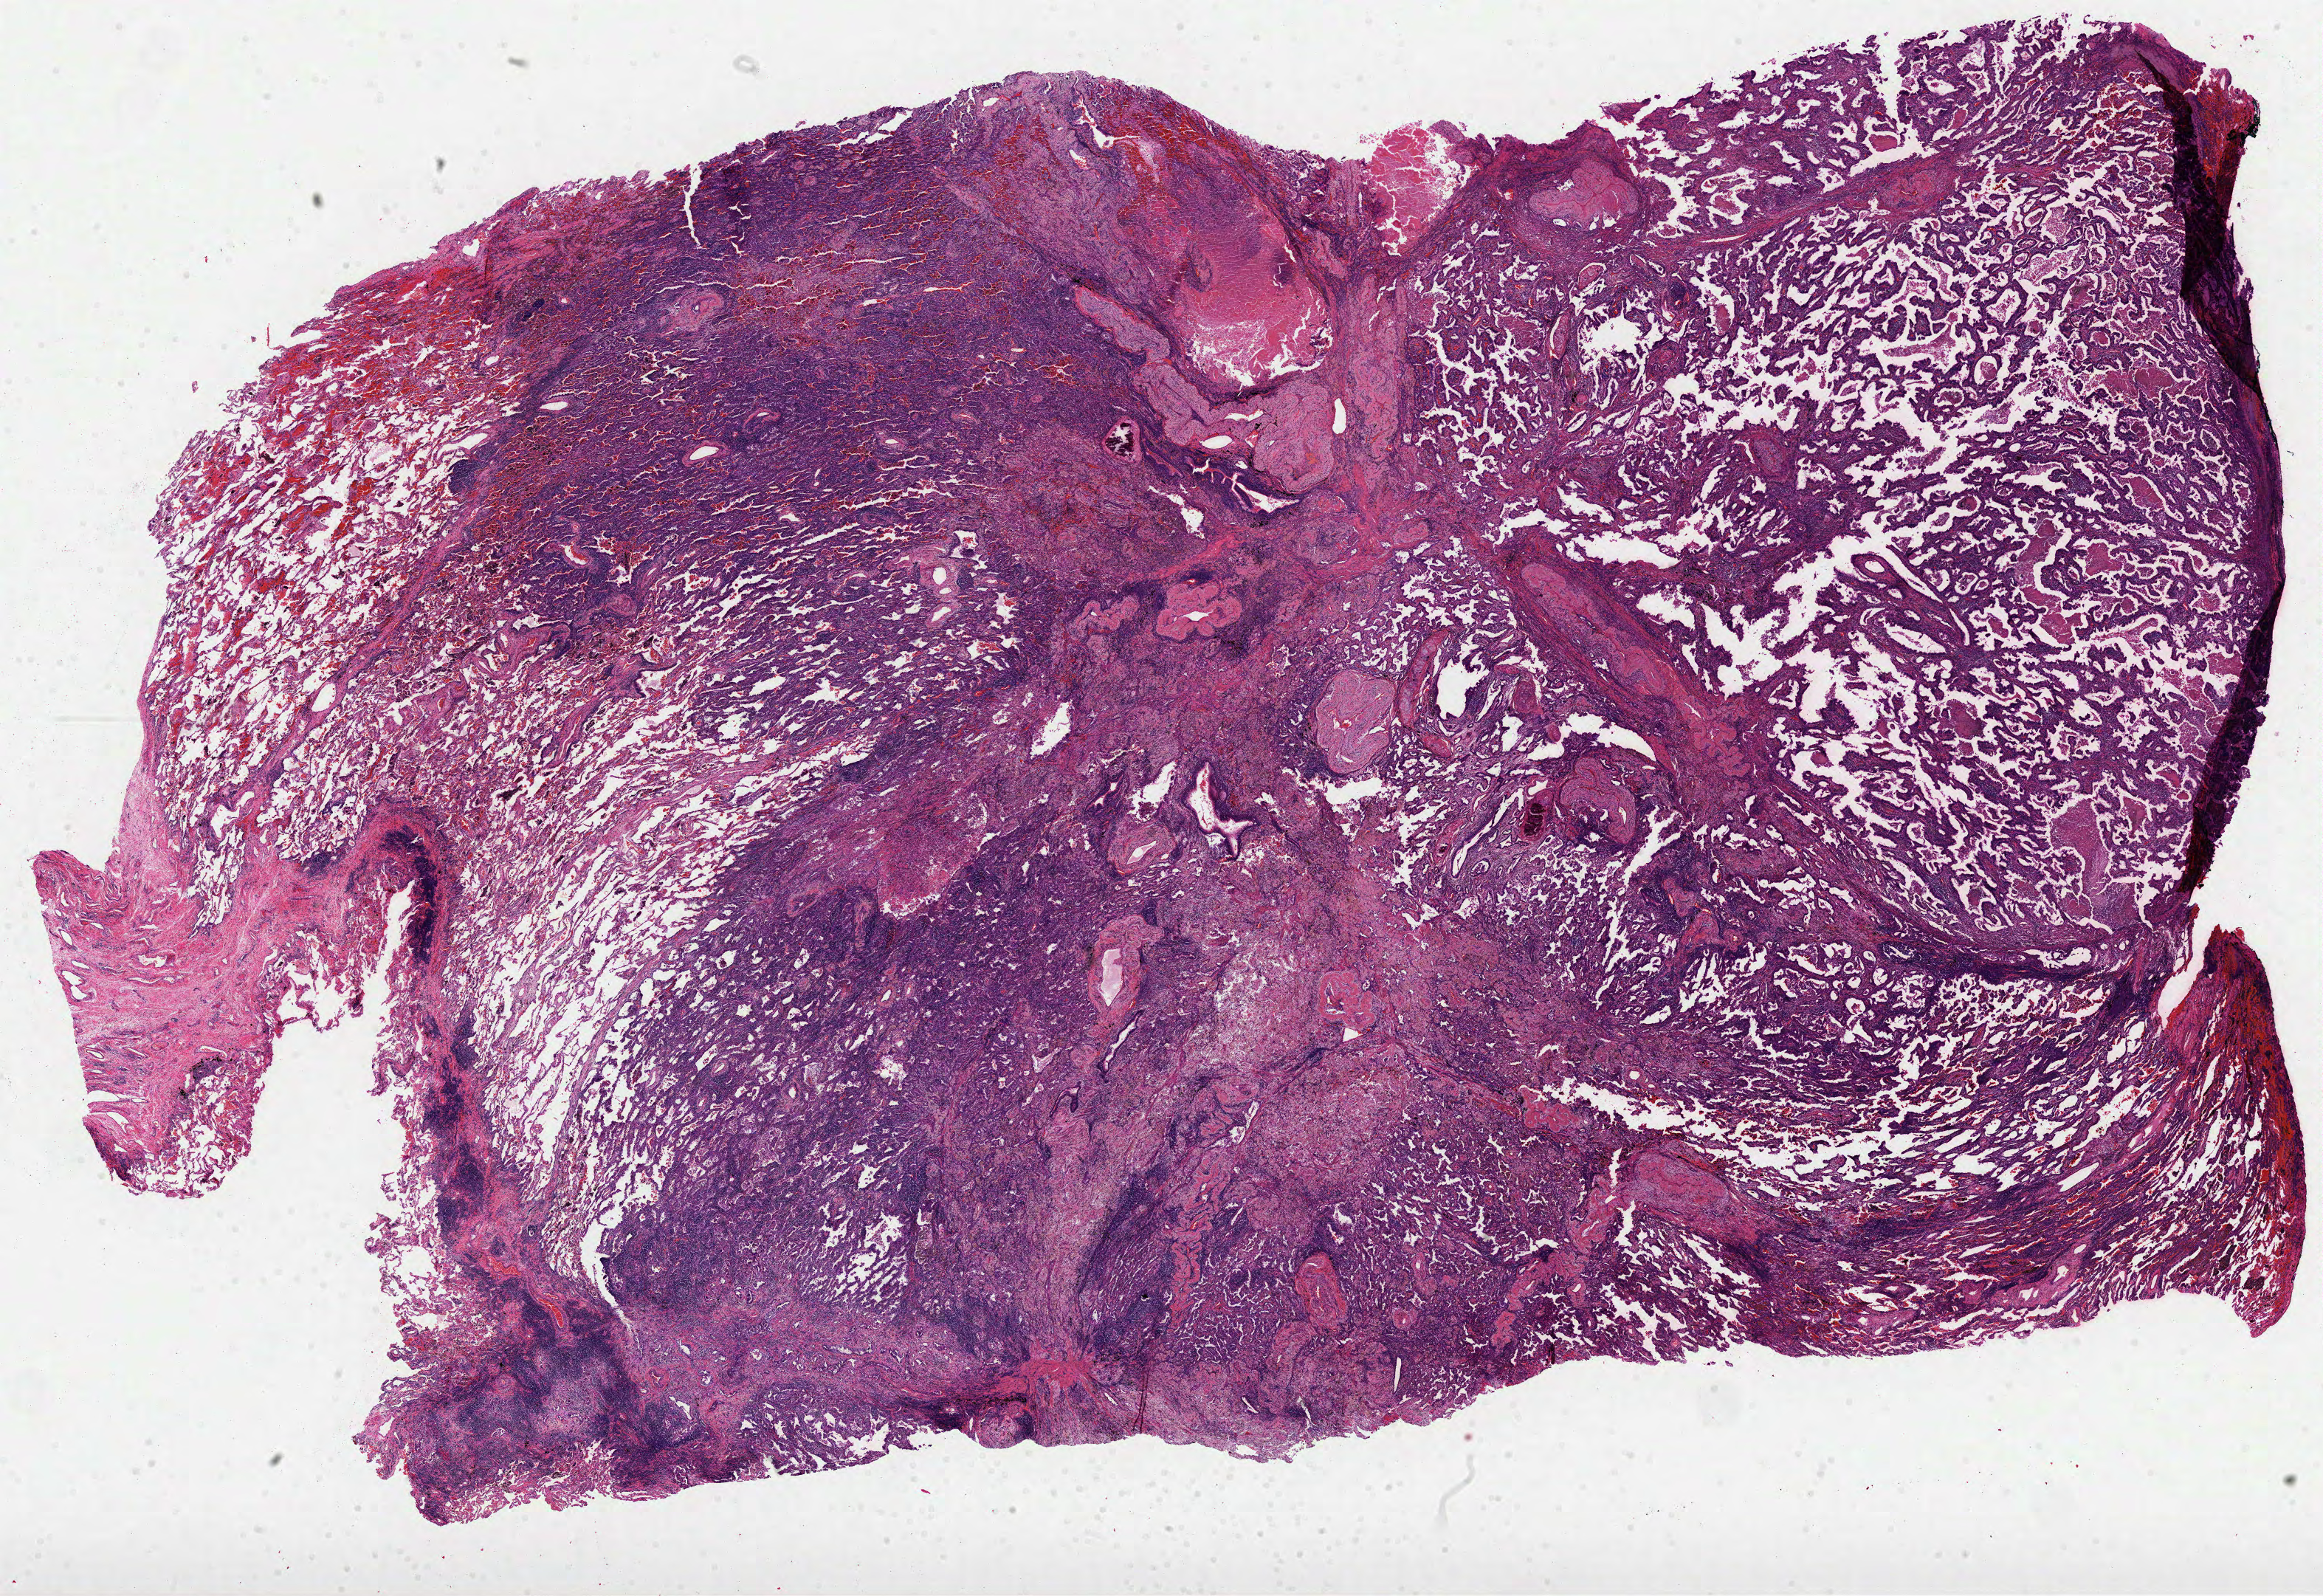
Whole-slide histology image, H&E-stained — shown as a low-resolution overview of the whole scanned area (about 25.4 x 17.4 mm). Formalin-fixed paraffin-embedded (FFPE) diagnostic section. Primary tumour sample from the lung. Patient: female, age at initial diagnosis 64 years.
AJCC pathologic stage: IIA. Diagnosis: Adenocarcinoma with mixed subtypes (upper lobe, lung). Laterality: left. TNM: T2a N1 MX.